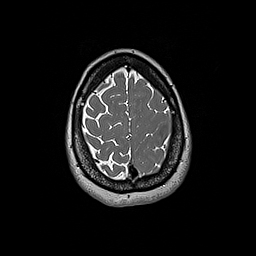
Brain MRI from a brain-tumour surgery series, one axial slice; slice 50 of 192 in the series (ordered by position); 1 mm slice thickness; 256 × 256 image matrix. Case-level facts recorded for this patient, not image findings: histopathology: Glioblastoma; WHO grade: 4; IDH mutation: no.
Structures marked on this image (manually delineated by an expert):
- tumour: box from (x=161, y=133) to (x=182, y=156) px